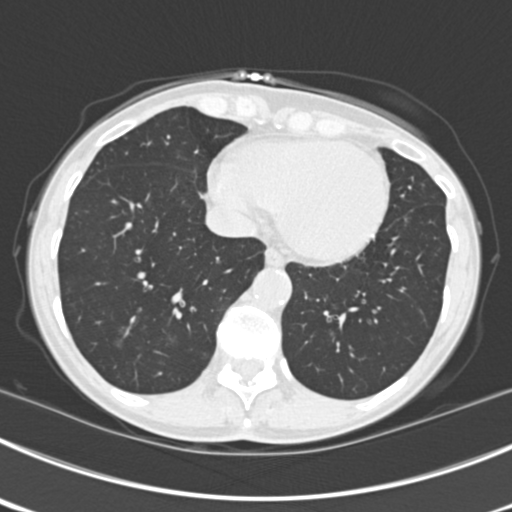
Chest CT (low-dose screening protocol), one axial image, third annual screen, lung window (W 1500 / L -600 HU), standard (soft-tissue) reconstruction kernel (B30f), slice 147 of 225 in the series, 512 × 512 image matrix. Female, age 63 years at enrolment. Current smoker at enrolment.
• Lesion marked by an expert reader, bounding box [x1, y1, x2, y2] px = [103, 309, 149, 356].
• The screening reader recorded 9 non-calcified nodules or masses ≥4 mm on this exam; which of them this box marks is not recorded.
• Official screen result: positive, other.
• Participant outcome: lung cancer diagnosed 15 days after this screen — bronchiolo-alveolar adenocarcinoma, NOS, right upper lobe, right middle lobe, right lower lobe, left upper lobe, left lower lobe, moderately differentiated (G2), stage IV (AJCC 6th edition).